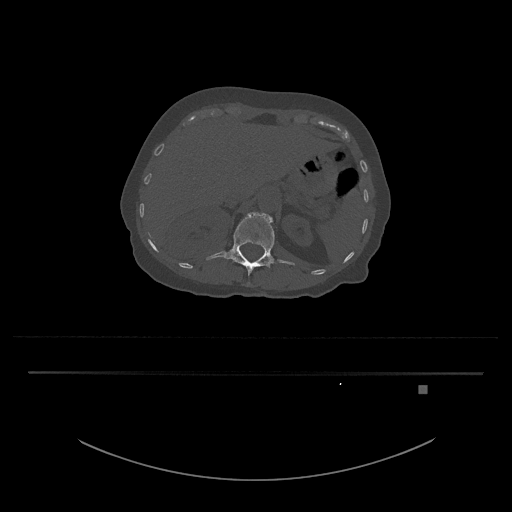
CT including the spine, one axial slice. Position 553 of 797 along the scan axis. 120 kVp. Bone window (W 1800 / L 400 HU). 0.5 mm slice thickness. 512 × 512 image matrix, field of view 500 × 500 mm. Patient: female, 57 years. From the clinical record (not read from this slice): primary cancer: cervical.
Structures marked on this image (semi-automatically segmented with operator editing):
- L1 vertebra: bounding box <206,212,295,276> (left, top, right, bottom; pixels)